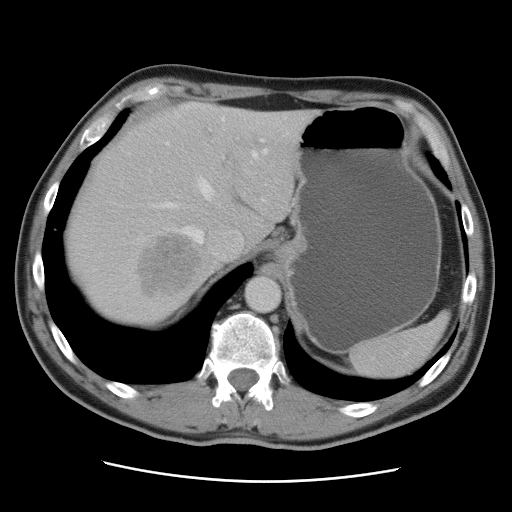
Contrast-enhanced abdominal CT, one axial slice. Position 70 of 89 along the scan axis. Soft-tissue window (W 400 / L 40 HU). 5 mm slice thickness. 512 × 512 image matrix, field of view 366 × 366 mm. Male patient, age 59 years. From the clinical record (not read from this slice): diagnosis: colorectal cancer liver metastases, imaged before liver resection; multiple liver metastases: yes; largest metastasis: 0.6 cm; disease in both lobes: yes.
Annotated regions visible in this slice (manually delineated by an expert):
- hepatic veins: bounding box <158,118,286,255> (left, top, right, bottom; pixels)
- liver: <63,103,314,328>
- planned liver remnant (the part of the liver to remain after resection): <112,103,315,243>
- portal vein (with intrahepatic branches): <223,139,264,158>
- liver metastasis: <140,235,201,295>